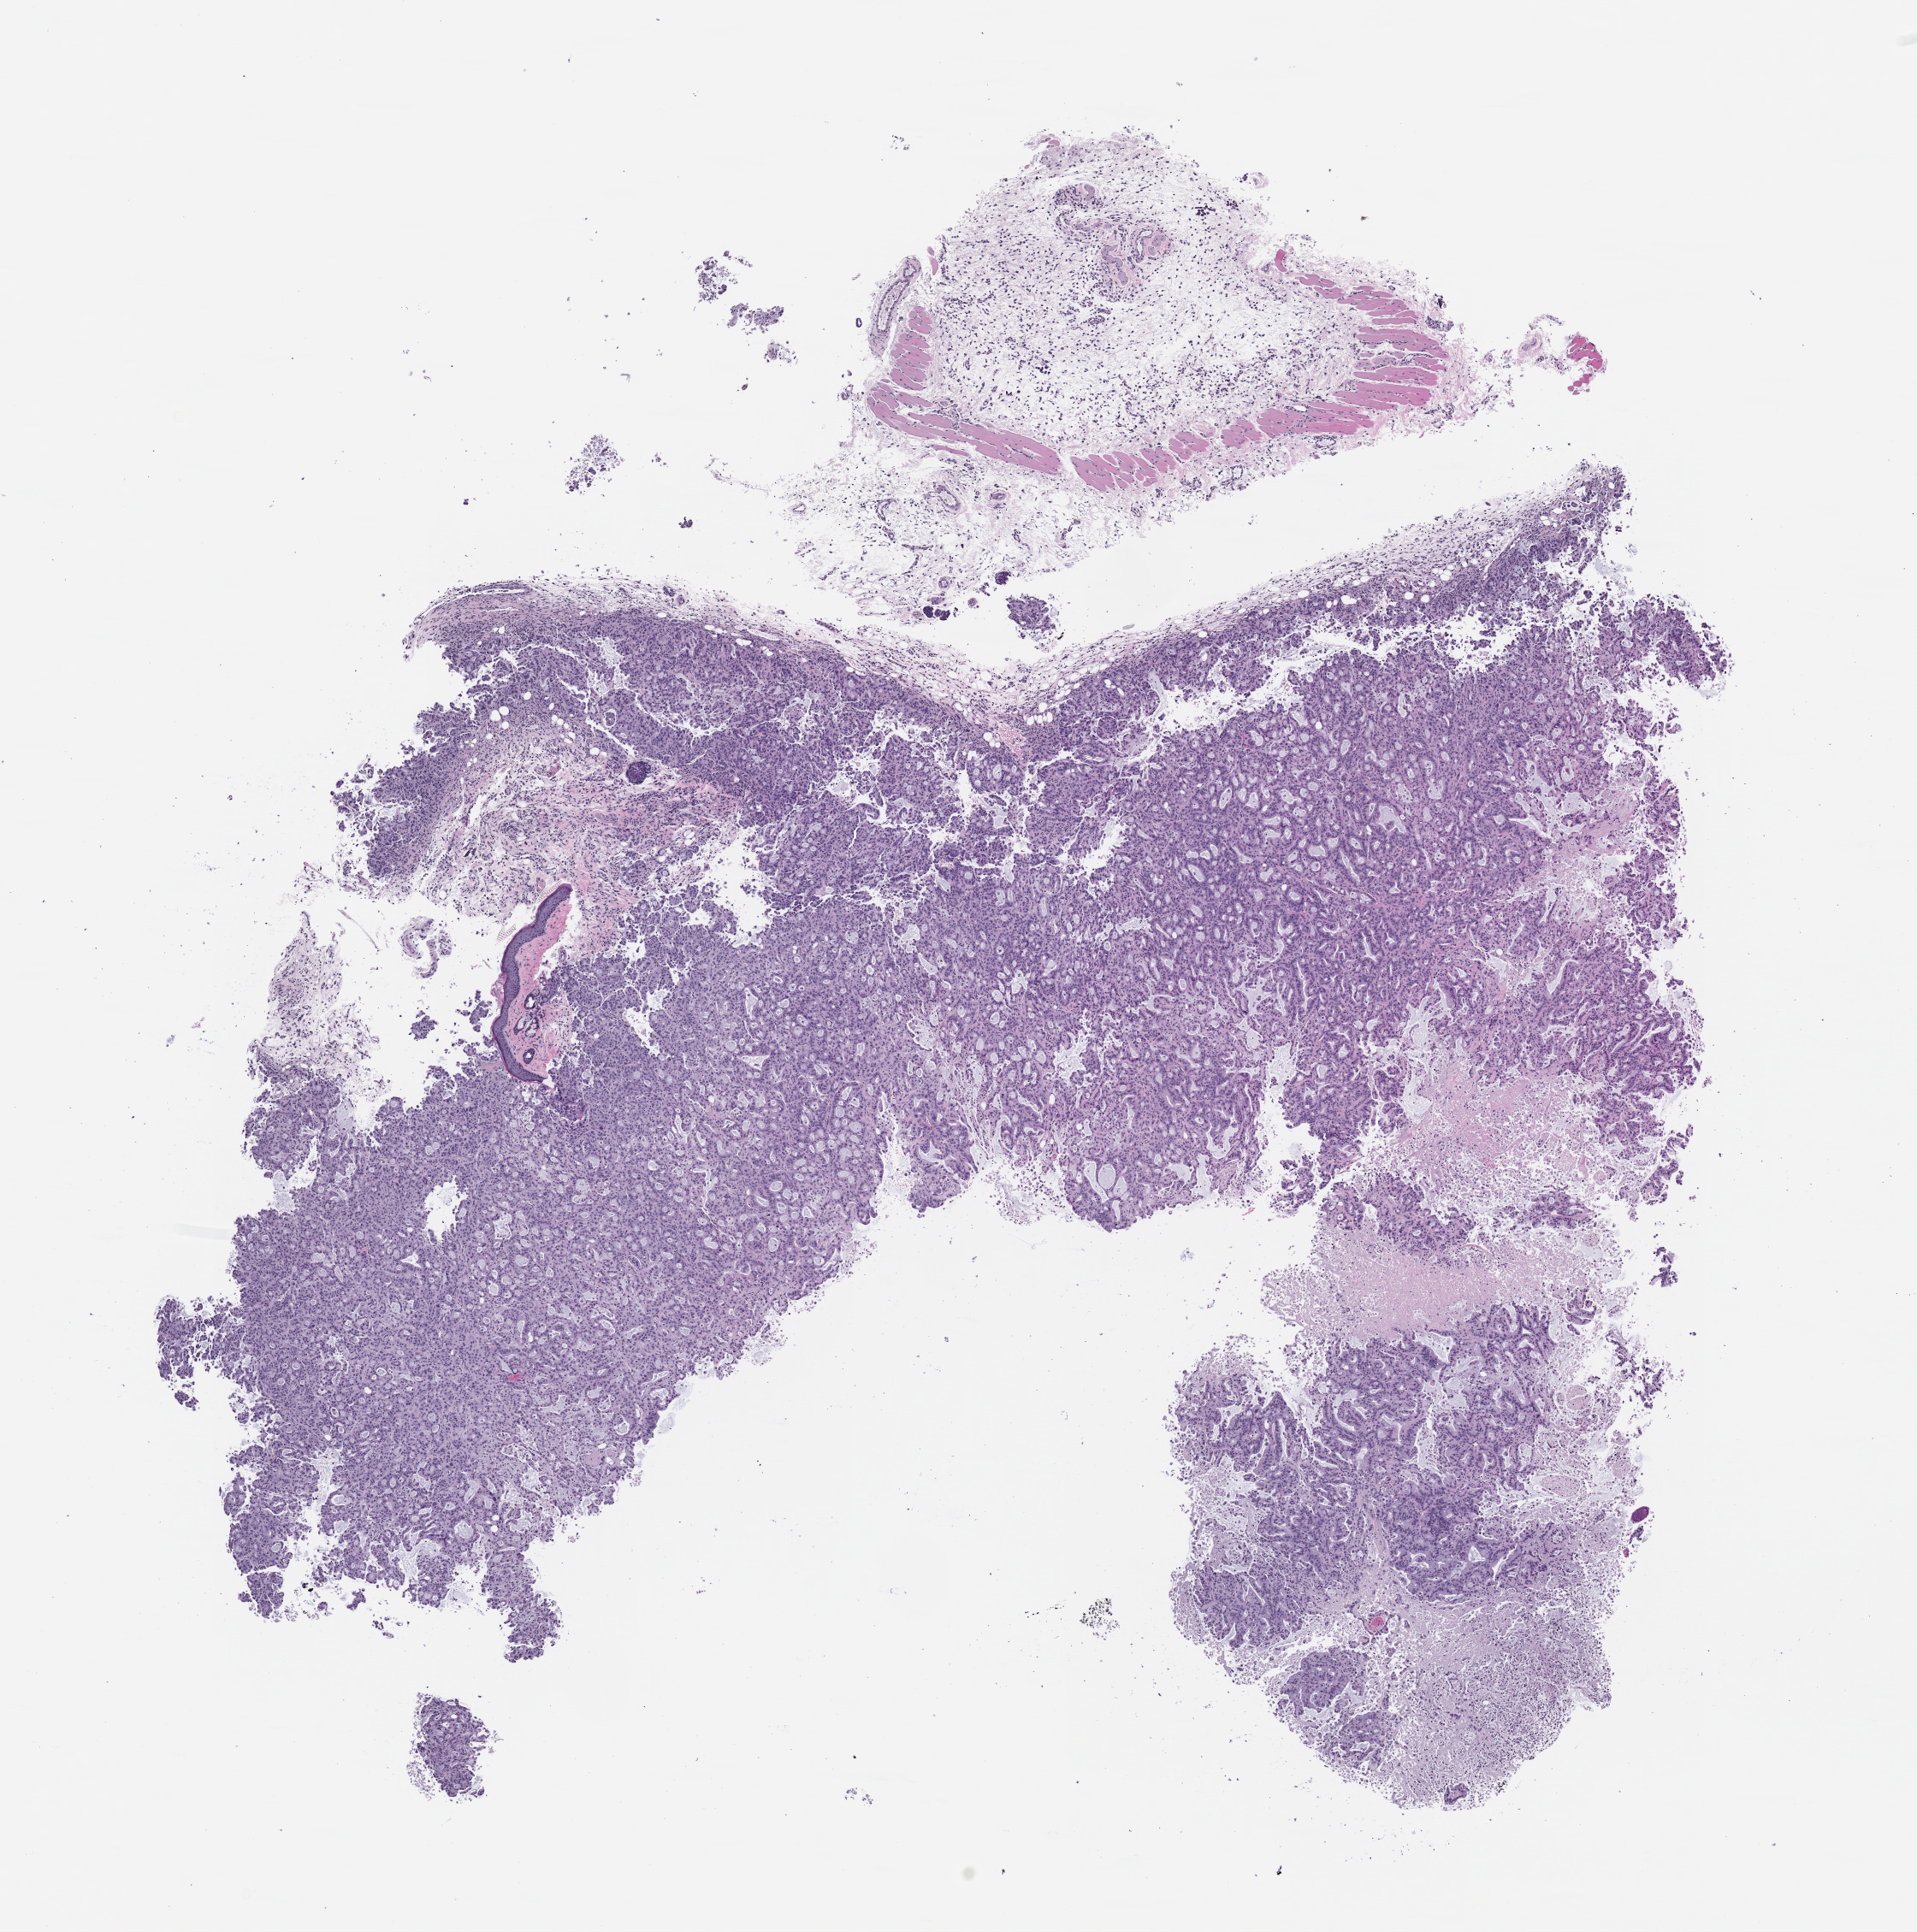
Whole-slide image, hematoxylin and eosin (H&E): patient-derived xenograft (human tumor grown in a mouse), passage 0 — a low-resolution overview of the entire scanned area, about 9.0 x 9.1 mm. Formalin-fixed, paraffin-embedded (FFPE) tissue. Originating tumor site category: pancreas.
• originating patient diagnosis: Pancreatic Adenocarcinoma